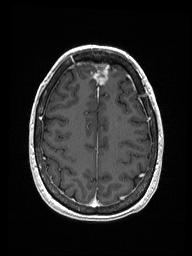
Brain MRI from a brain-tumour surgery series, one axial slice. T1-weighted post-contrast. 1 mm slice thickness. 192 × 256 image matrix, field of view 187 × 250 mm. From the clinical record (not read from this slice): histopathology: Metastastic Carcinoma from Breast primary; tumour location: Right Frontal.
Outlined on this slice (expert manual segmentation):
- previous resection cavity: bounding box <95,63,110,85> (left, top, right, bottom; pixels)